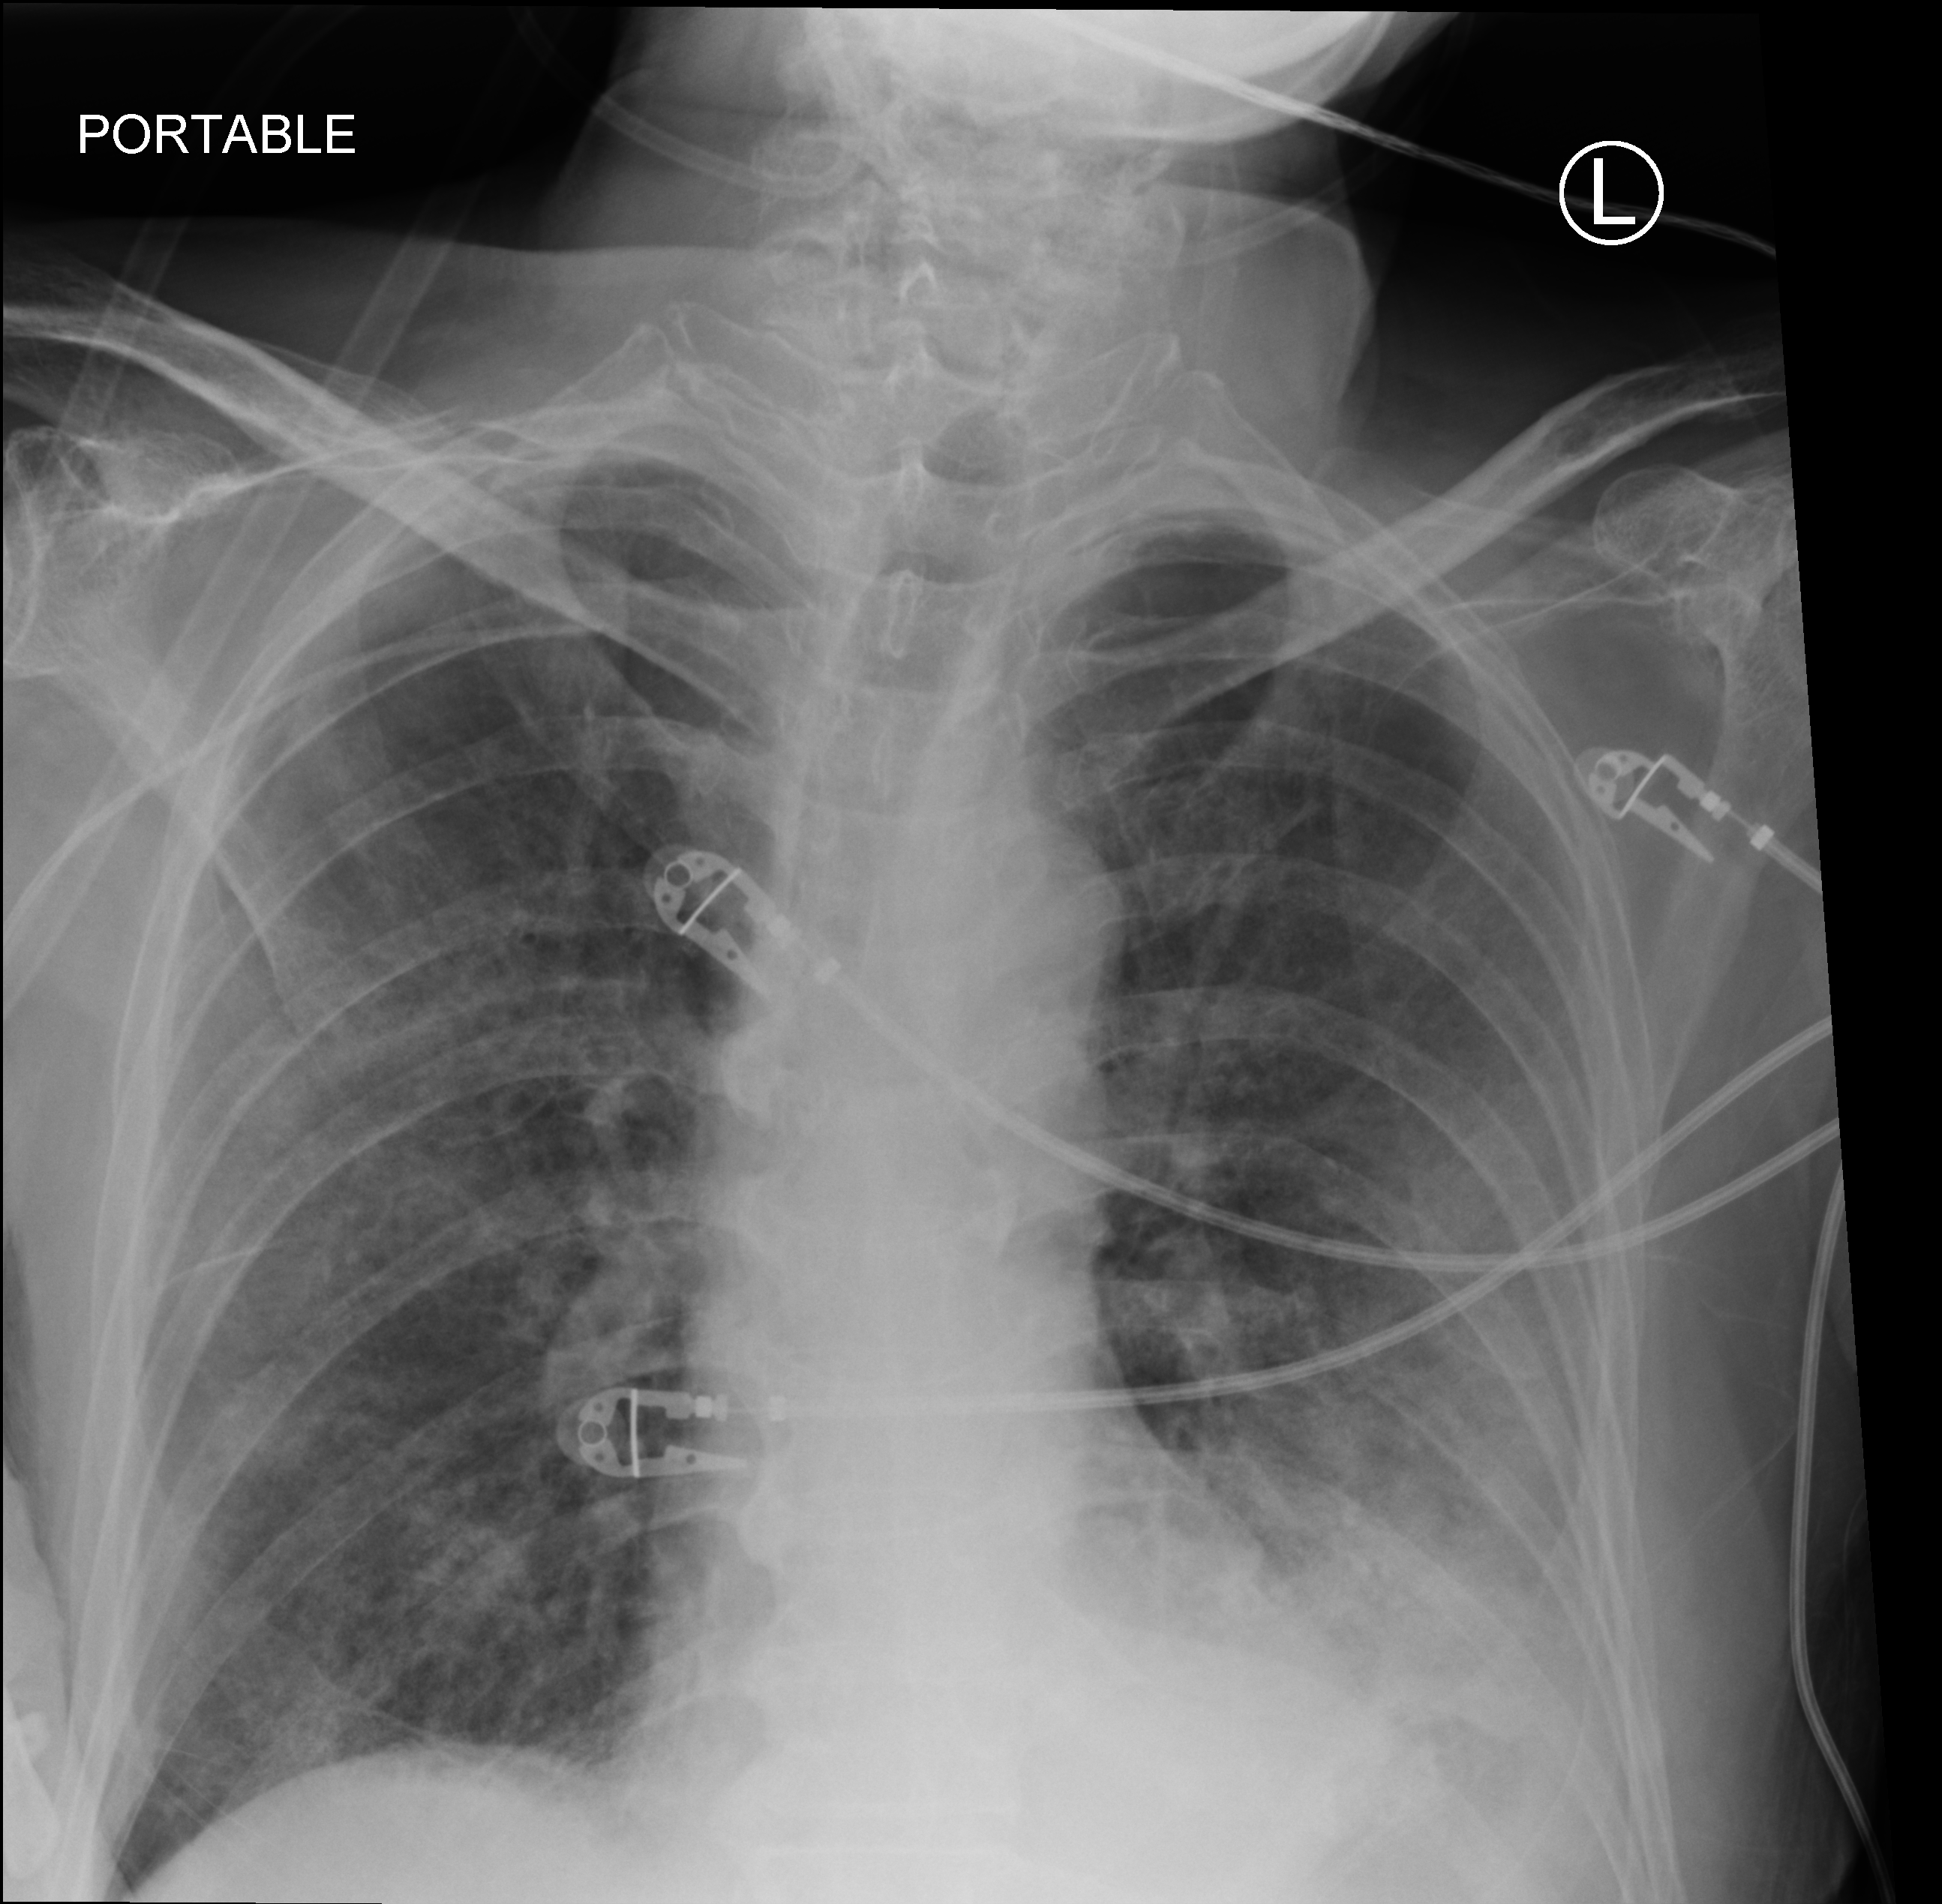
Portable chest radiograph; anteroposterior (AP) projection. Patient hospitalised with COVID-19; male, aged 60–74 years.
Admission-level facts for this patient (not findings on this image; timing relative to this image not recorded):
- mechanically ventilated during this hospital stay: yes
- admitted to intensive care during this hospital stay: yes